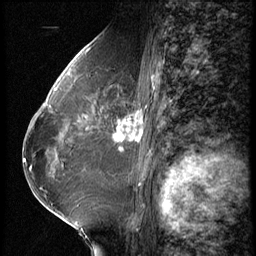
Breast MRI (dynamic contrast-enhanced), one sagittal slice; slice 32 of 62 in the series (ordered by position); 3 images stored at this slice position (order not interpretable as contrast timing); 1.5 T; TE 4.2 ms, TR 9 ms; 2.5 mm slice thickness; 256 × 256 image matrix, field of view 180 × 180 mm. Patient: female, 65 years. Case-level facts recorded for this patient, not image findings: setting: breast cancer imaged before/during neoadjuvant chemotherapy; receptor status: HR-positive, HER2-negative.
Annotated regions visible in this slice (semi-automatic segmentation, software-assisted and operator-edited):
- analysis volume of interest (the breast-tissue region the enhancement analysis was run in; not a lesion): bounding box [x1, y1, x2, y2] px = [104, 104, 154, 161]
- tumour enhancement mask (voxels above the 140 % enhancement threshold inside the analysis volume of interest): [114, 110, 144, 141]